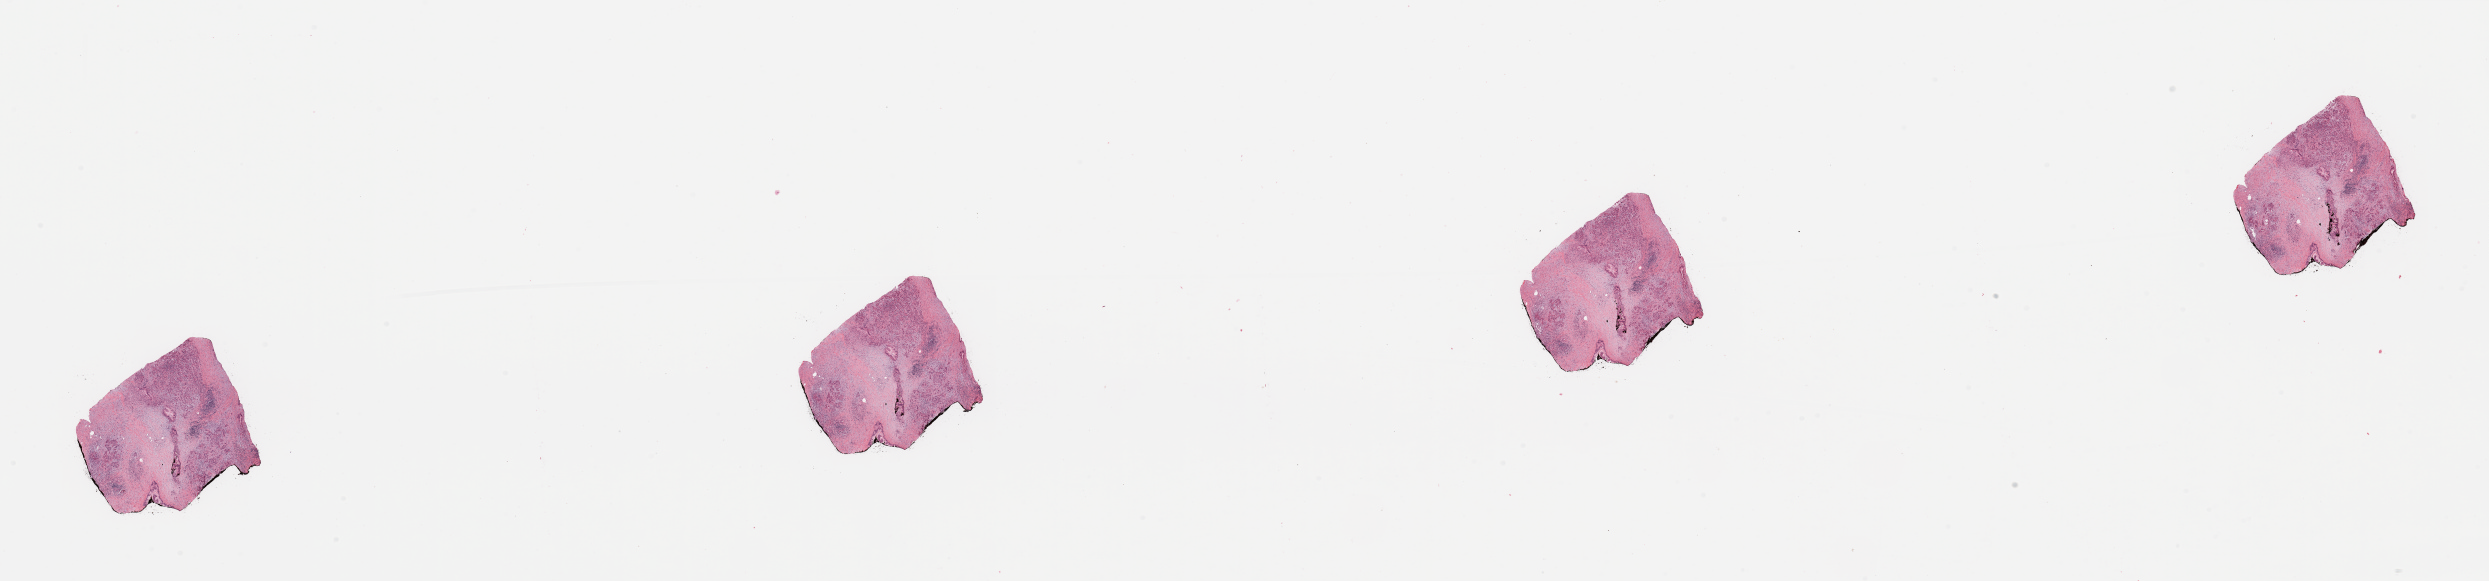
Whole-slide histology image, H&E, shown as a low-resolution overview of the whole scanned area (about 39.4 x 9.2 mm, acquisition: 20x scan); tumour tissue sample, sampled site: pancreas. 66-year-old male patient. Histologic grade: G2 (moderately differentiated). Composition of this section per pathologist review: tumour nuclei 15%, necrosis 0%.
AJCC pathologic stage: IIB. Histologic diagnosis: Infiltrating duct carcinoma, NOS. Primary tumour site (as recorded): head.